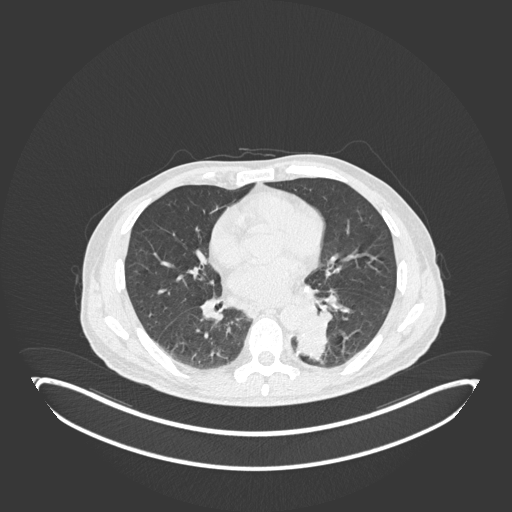
Chest CT, one axial slice. Position 85 of 251 along the scan axis. Reconstruction kernel B30f. 120 kVp. Lung window (W 1500 / L -600 HU). 1 mm slice thickness. 512 × 512 image matrix. Patient: male, 72 years. Case-level facts recorded for this patient, not image findings: clinical TNM (as recorded): T2b N0 M1.
Annotated regions visible in this slice (bounding box drawn by a radiologist):
- lung tumour (recorded histology: adenocarcinoma): box from (x=287, y=308) to (x=333, y=362) px